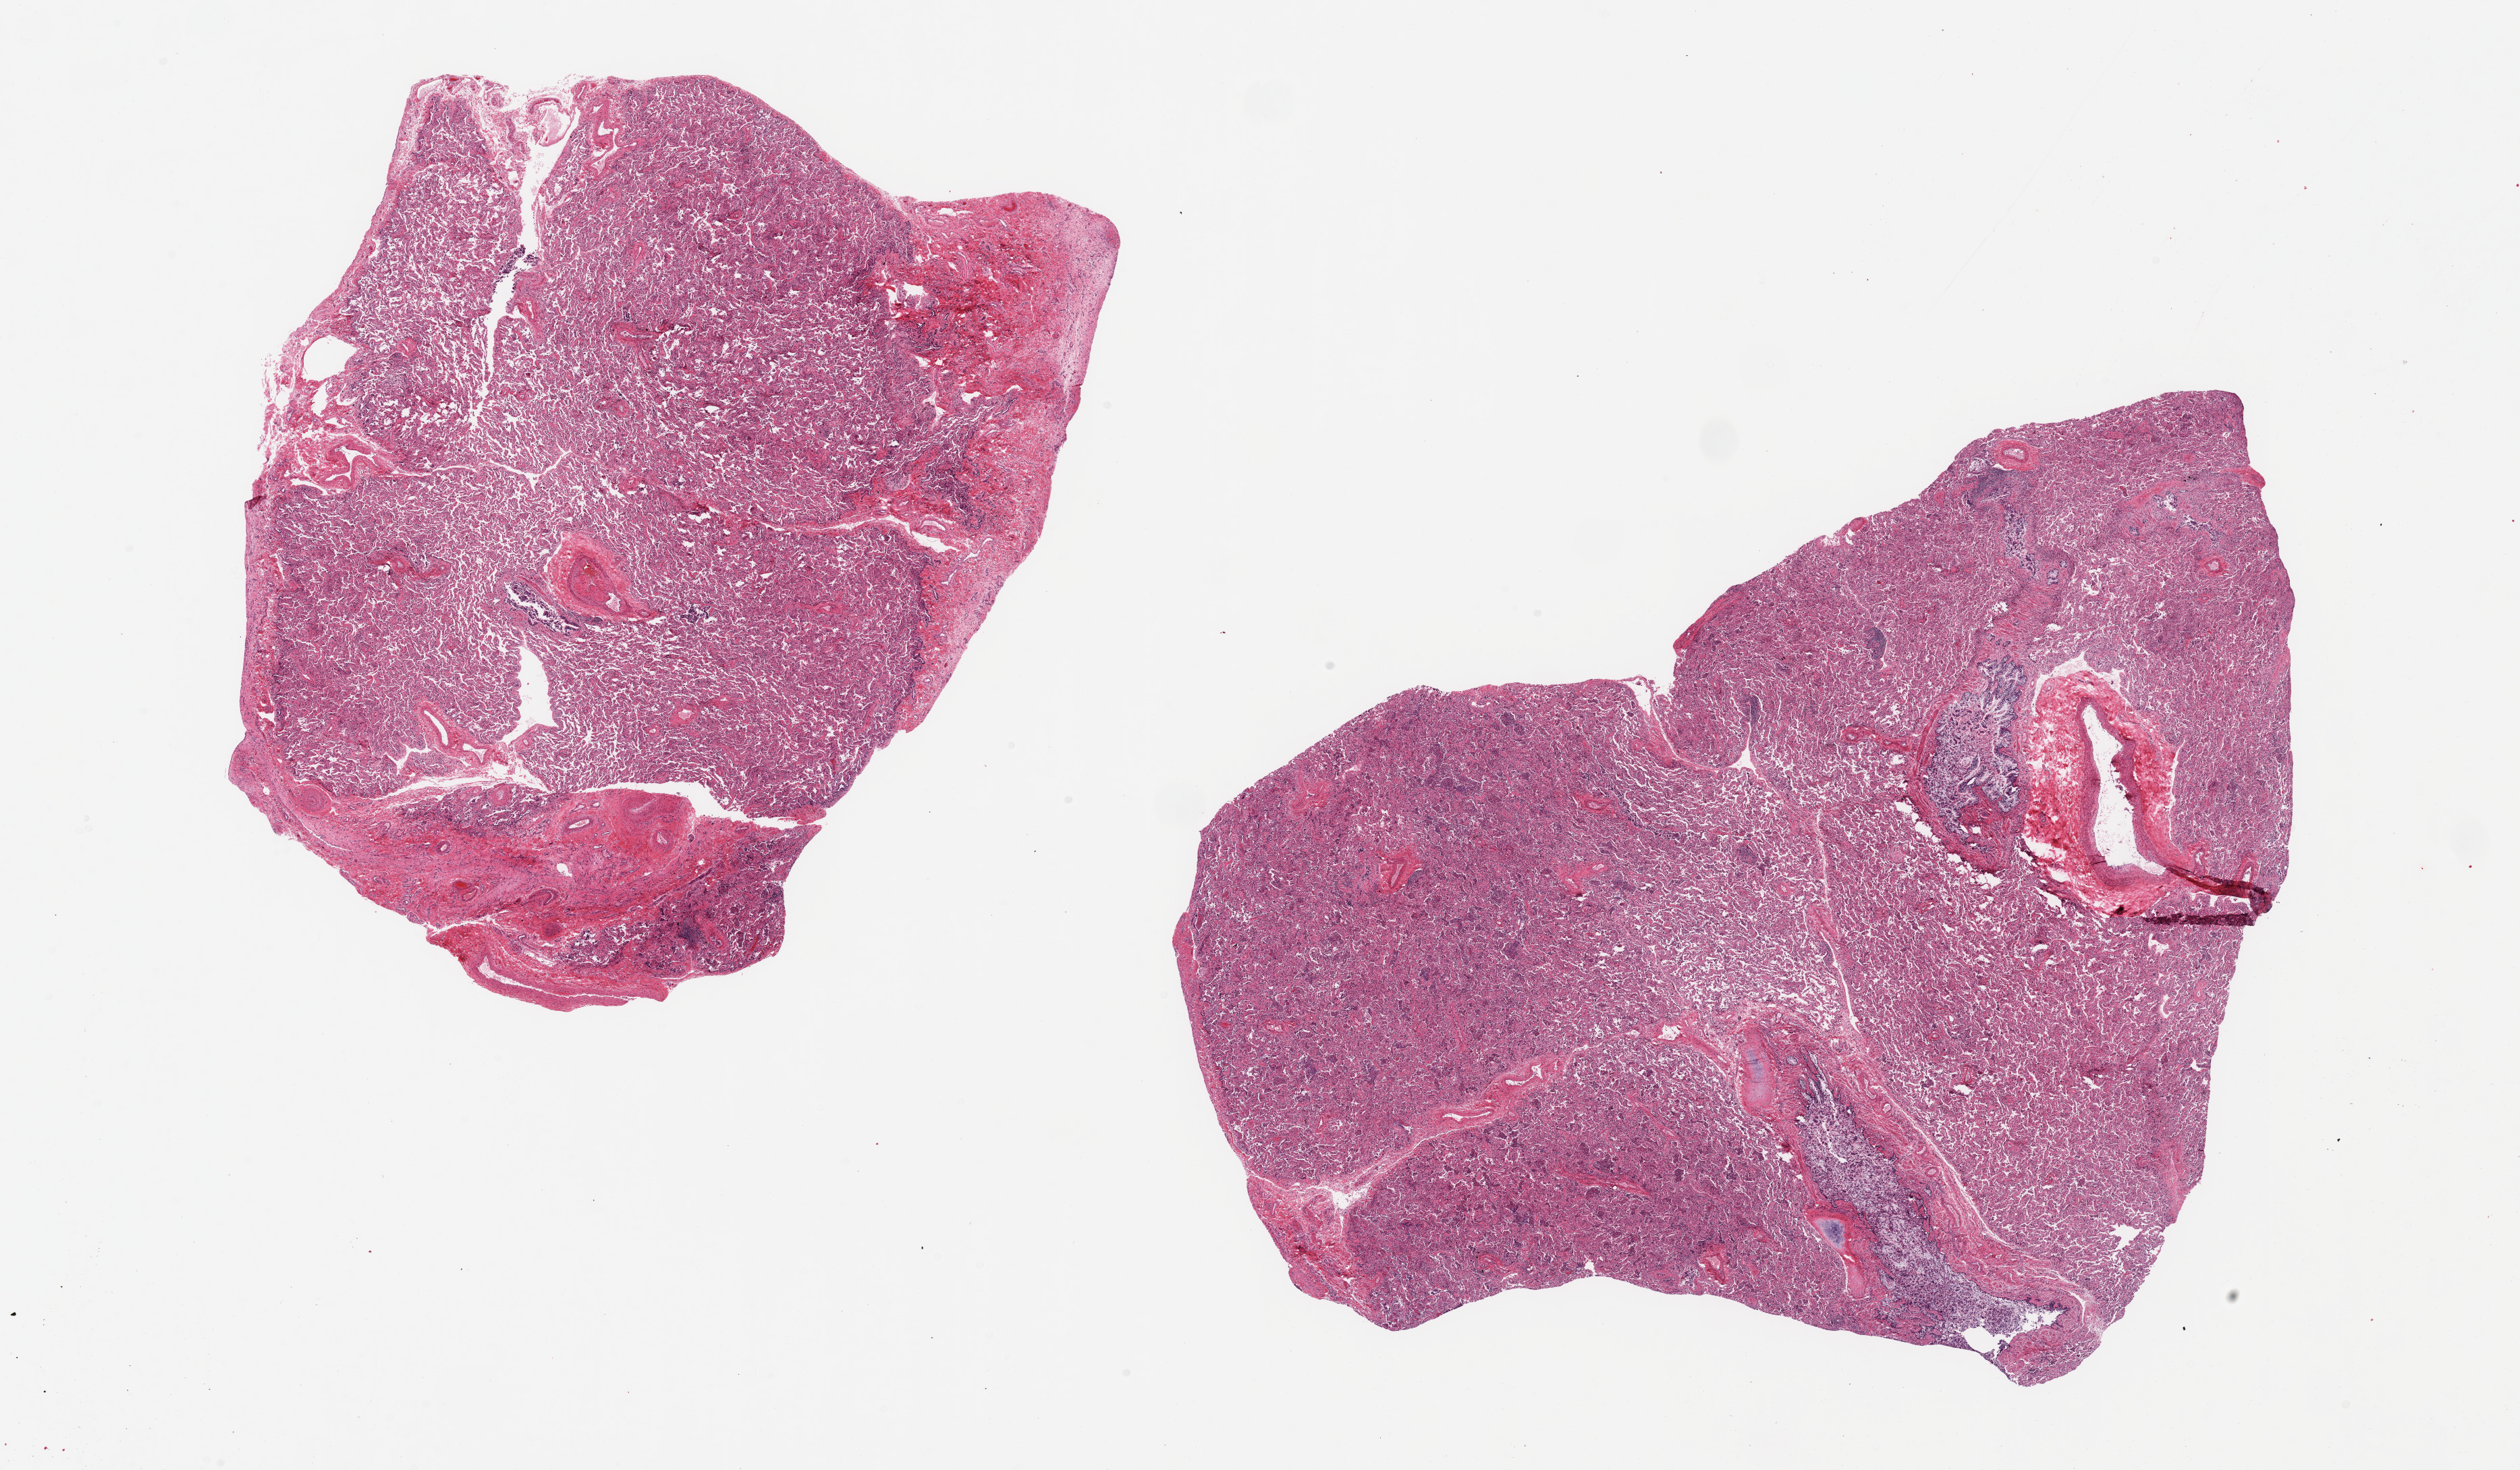
Digitized H&E-stained section, brightfield, a low-resolution overview of the entire scanned area, about 29.5 x 17.2 mm (slide scanned at 20x). PAXgene-fixed, paraffin-embedded tissue. Section of lung (target tissue). Donor tissue sample.
Reviewer comment on this tissue sample: 2 pieces; acute and organizing pneumonia, fibrosis, includes larger vessels/bronchi.